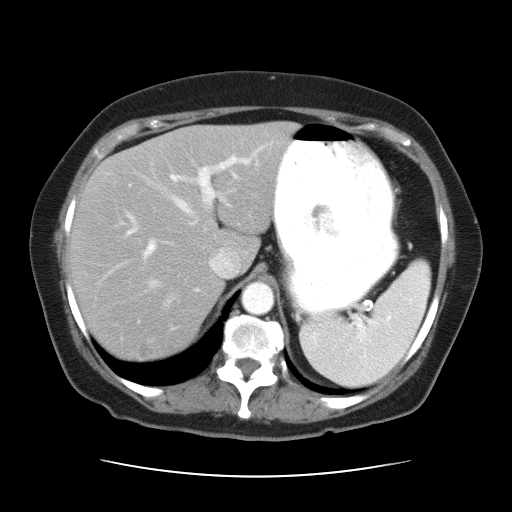
Contrast-enhanced abdominal CT, one axial slice; position 24 of 34 along the scan axis; reconstruction kernel STANDARD; intravenous contrast given; soft-tissue window (W 400 / L 40 HU); 7.5 mm slice thickness; 512 × 512 image matrix, field of view 360 × 360 mm. Female patient, age 65 years. Case-level facts recorded for this patient, not image findings: diagnosis: colorectal cancer liver metastases, imaged before liver resection; multiple liver metastases: yes; largest metastasis: 2.2 cm; disease in both lobes: no.
Annotated regions visible in this slice (outlined manually by an expert reader):
- hepatic veins: bounding box (x1, y1, x2, y2) in pixels: (115, 157, 260, 305)
- liver: (72, 123, 292, 359)
- planned liver remnant (the part of the liver to remain after resection): (72, 123, 292, 346)
- portal vein (with intrahepatic branches): (127, 146, 264, 257)
- liver metastasis: (136, 342, 154, 359)